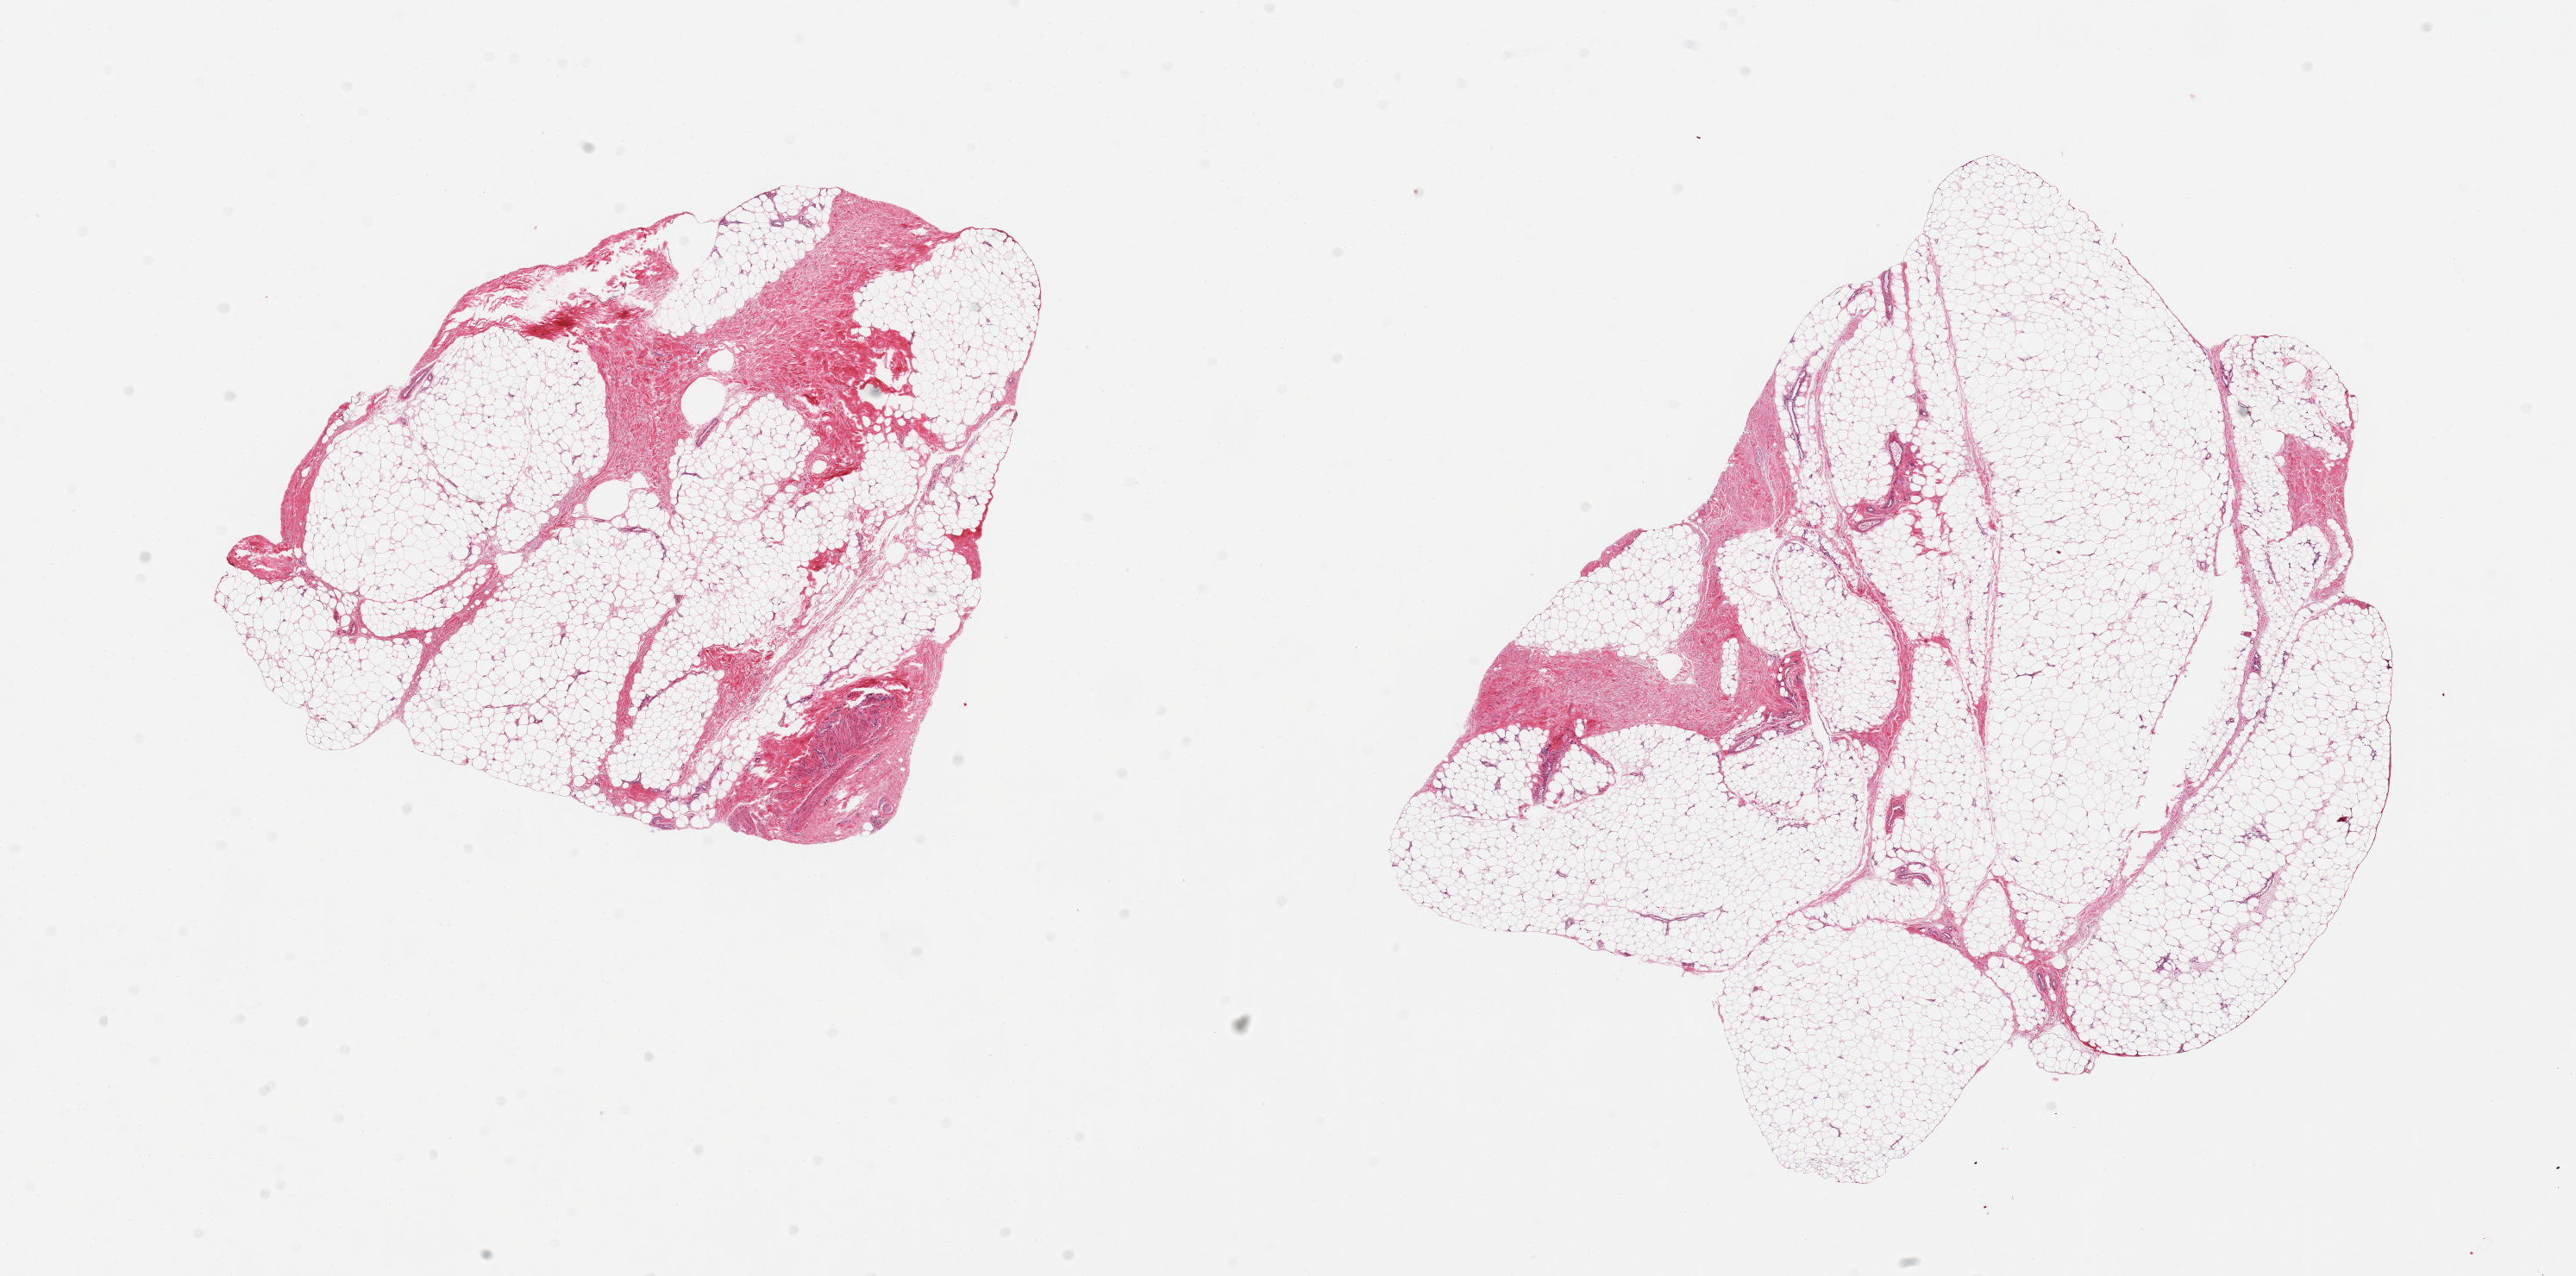
Digitized H&E-stained section, low-resolution overview of the scanned area, about 23.6 x 11.7 mm (from a 20x scan); PAXgene-fixed, paraffin-embedded tissue; section of adipose tissue (target tissue); tissue donor sample. Donor: male.
Reviewer comment on this tissue sample: 2 pieces; 20% fibrous content.